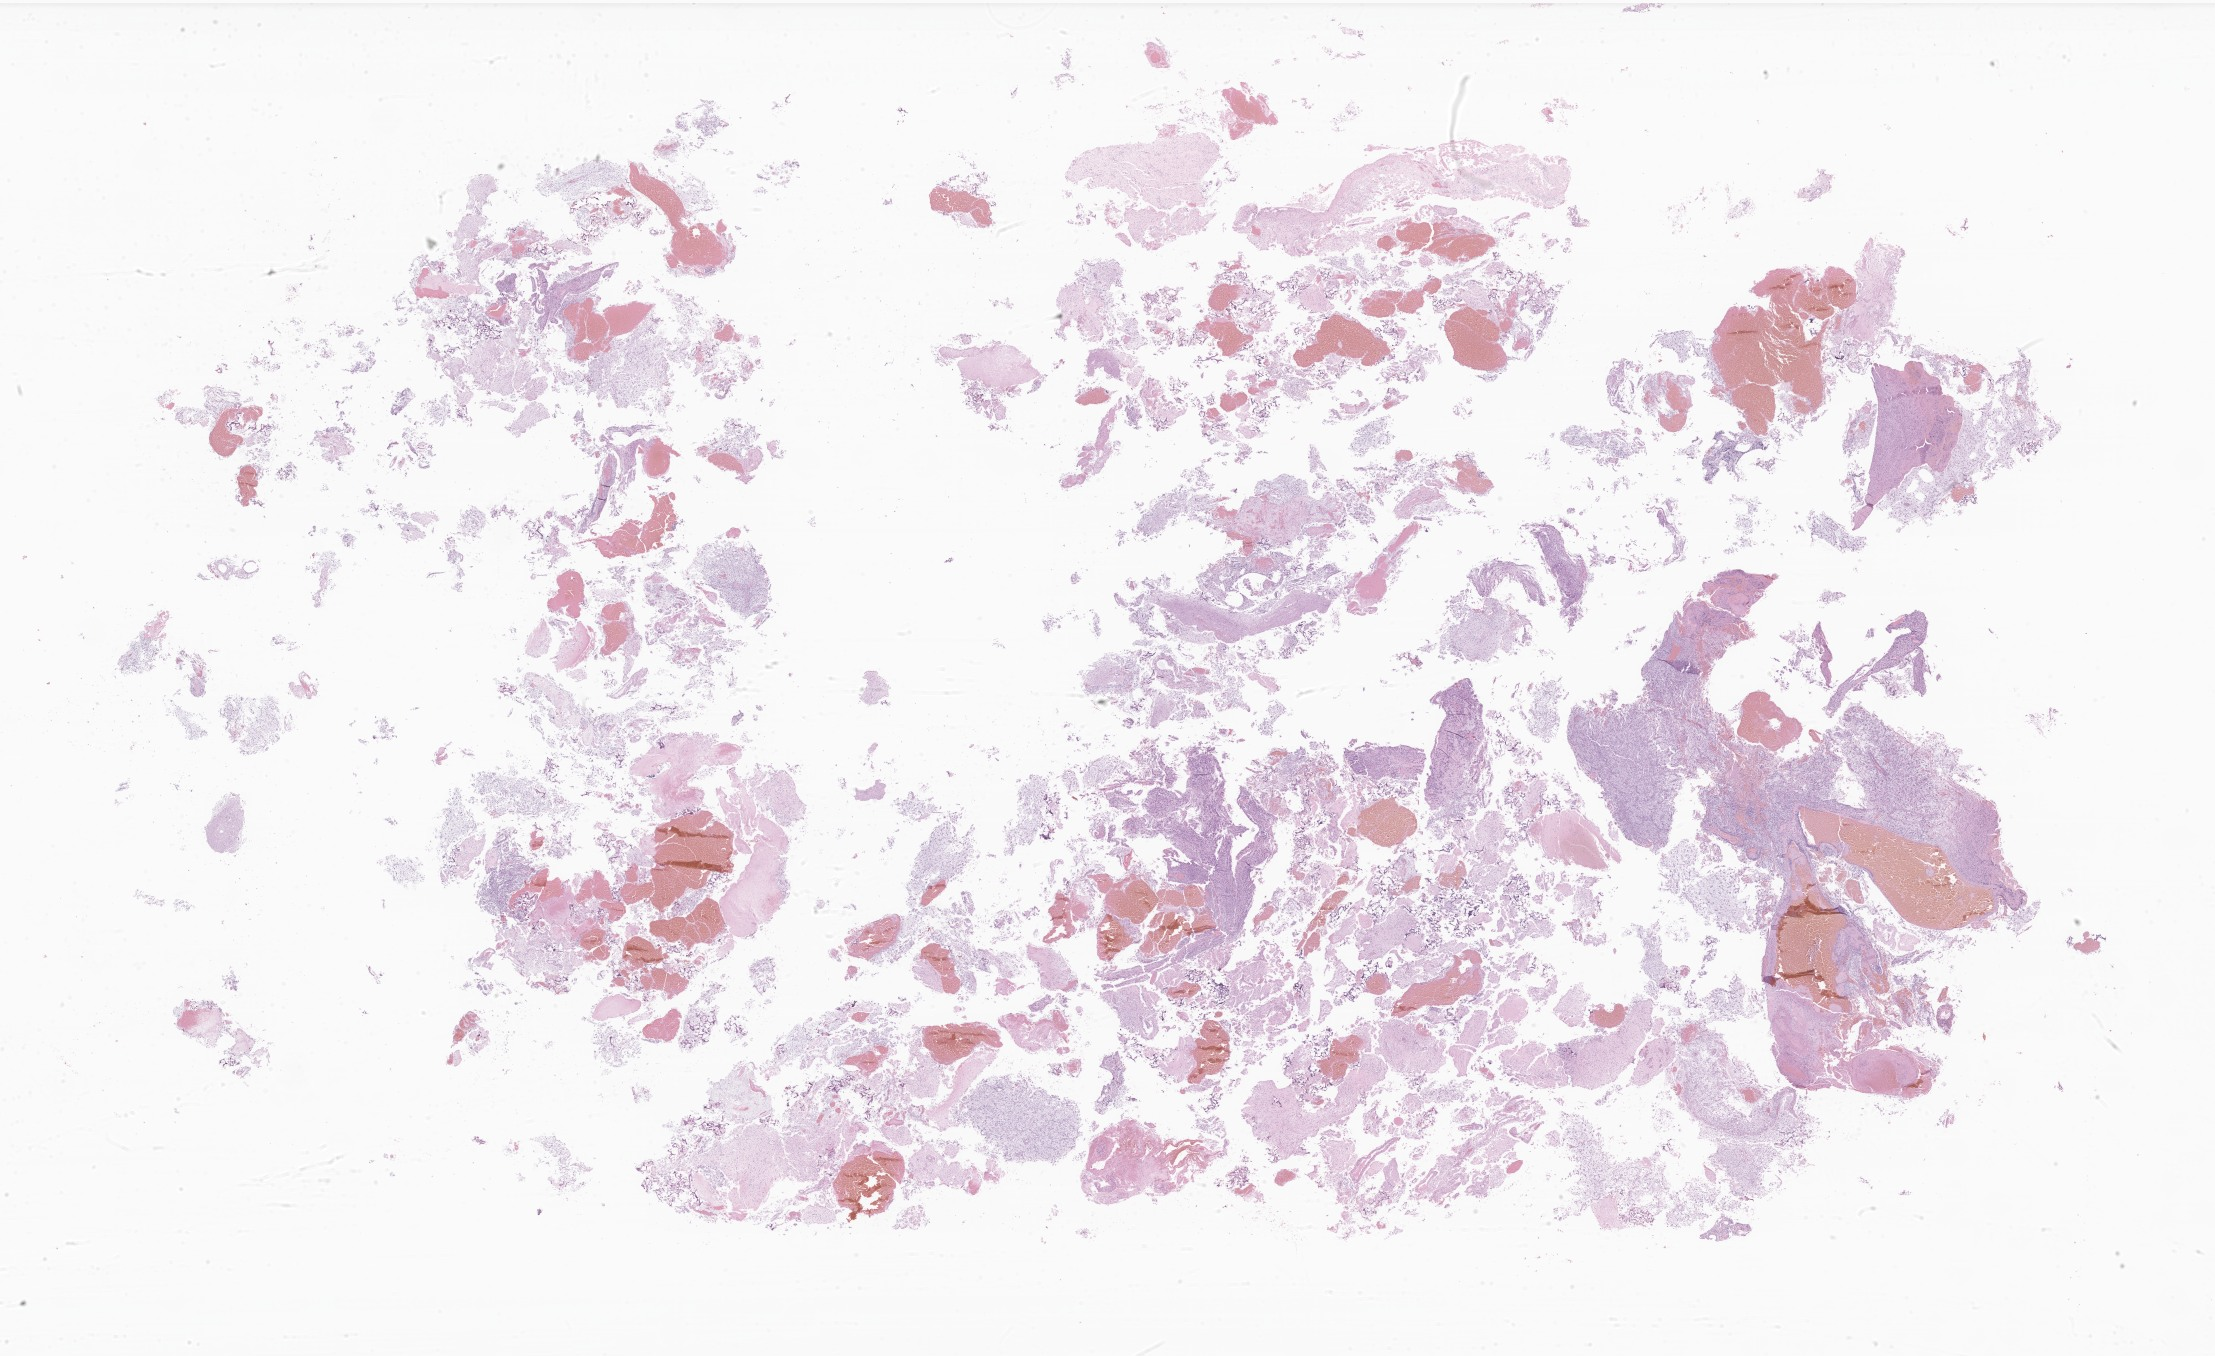
Digitized H&E-stained section of tumor tissue from the brain — low-resolution overview of the scanned area, about 37.4 x 22.9 mm. Patient female; age 189 months (15 years 9 months).
• specimen: formalin-fixed paraffin-embedded section